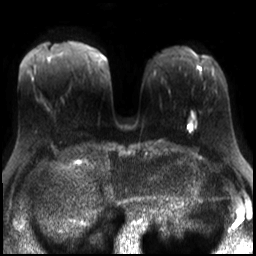
Breast MRI, one axial slice. Slice 12 of 30 in the series (ordered by position). Diffusion-weighted series; image 2 of 4 stored at this slice position (different b-values; order by instance number). 3 T. 4 mm slice thickness. 256 × 256 image matrix, field of view 320 × 320 mm. Female patient.
Outlined on this slice (manually delineated by an expert):
- tumour on diffusion-weighted imaging: bounding box <188,119,194,129> (left, top, right, bottom; pixels)